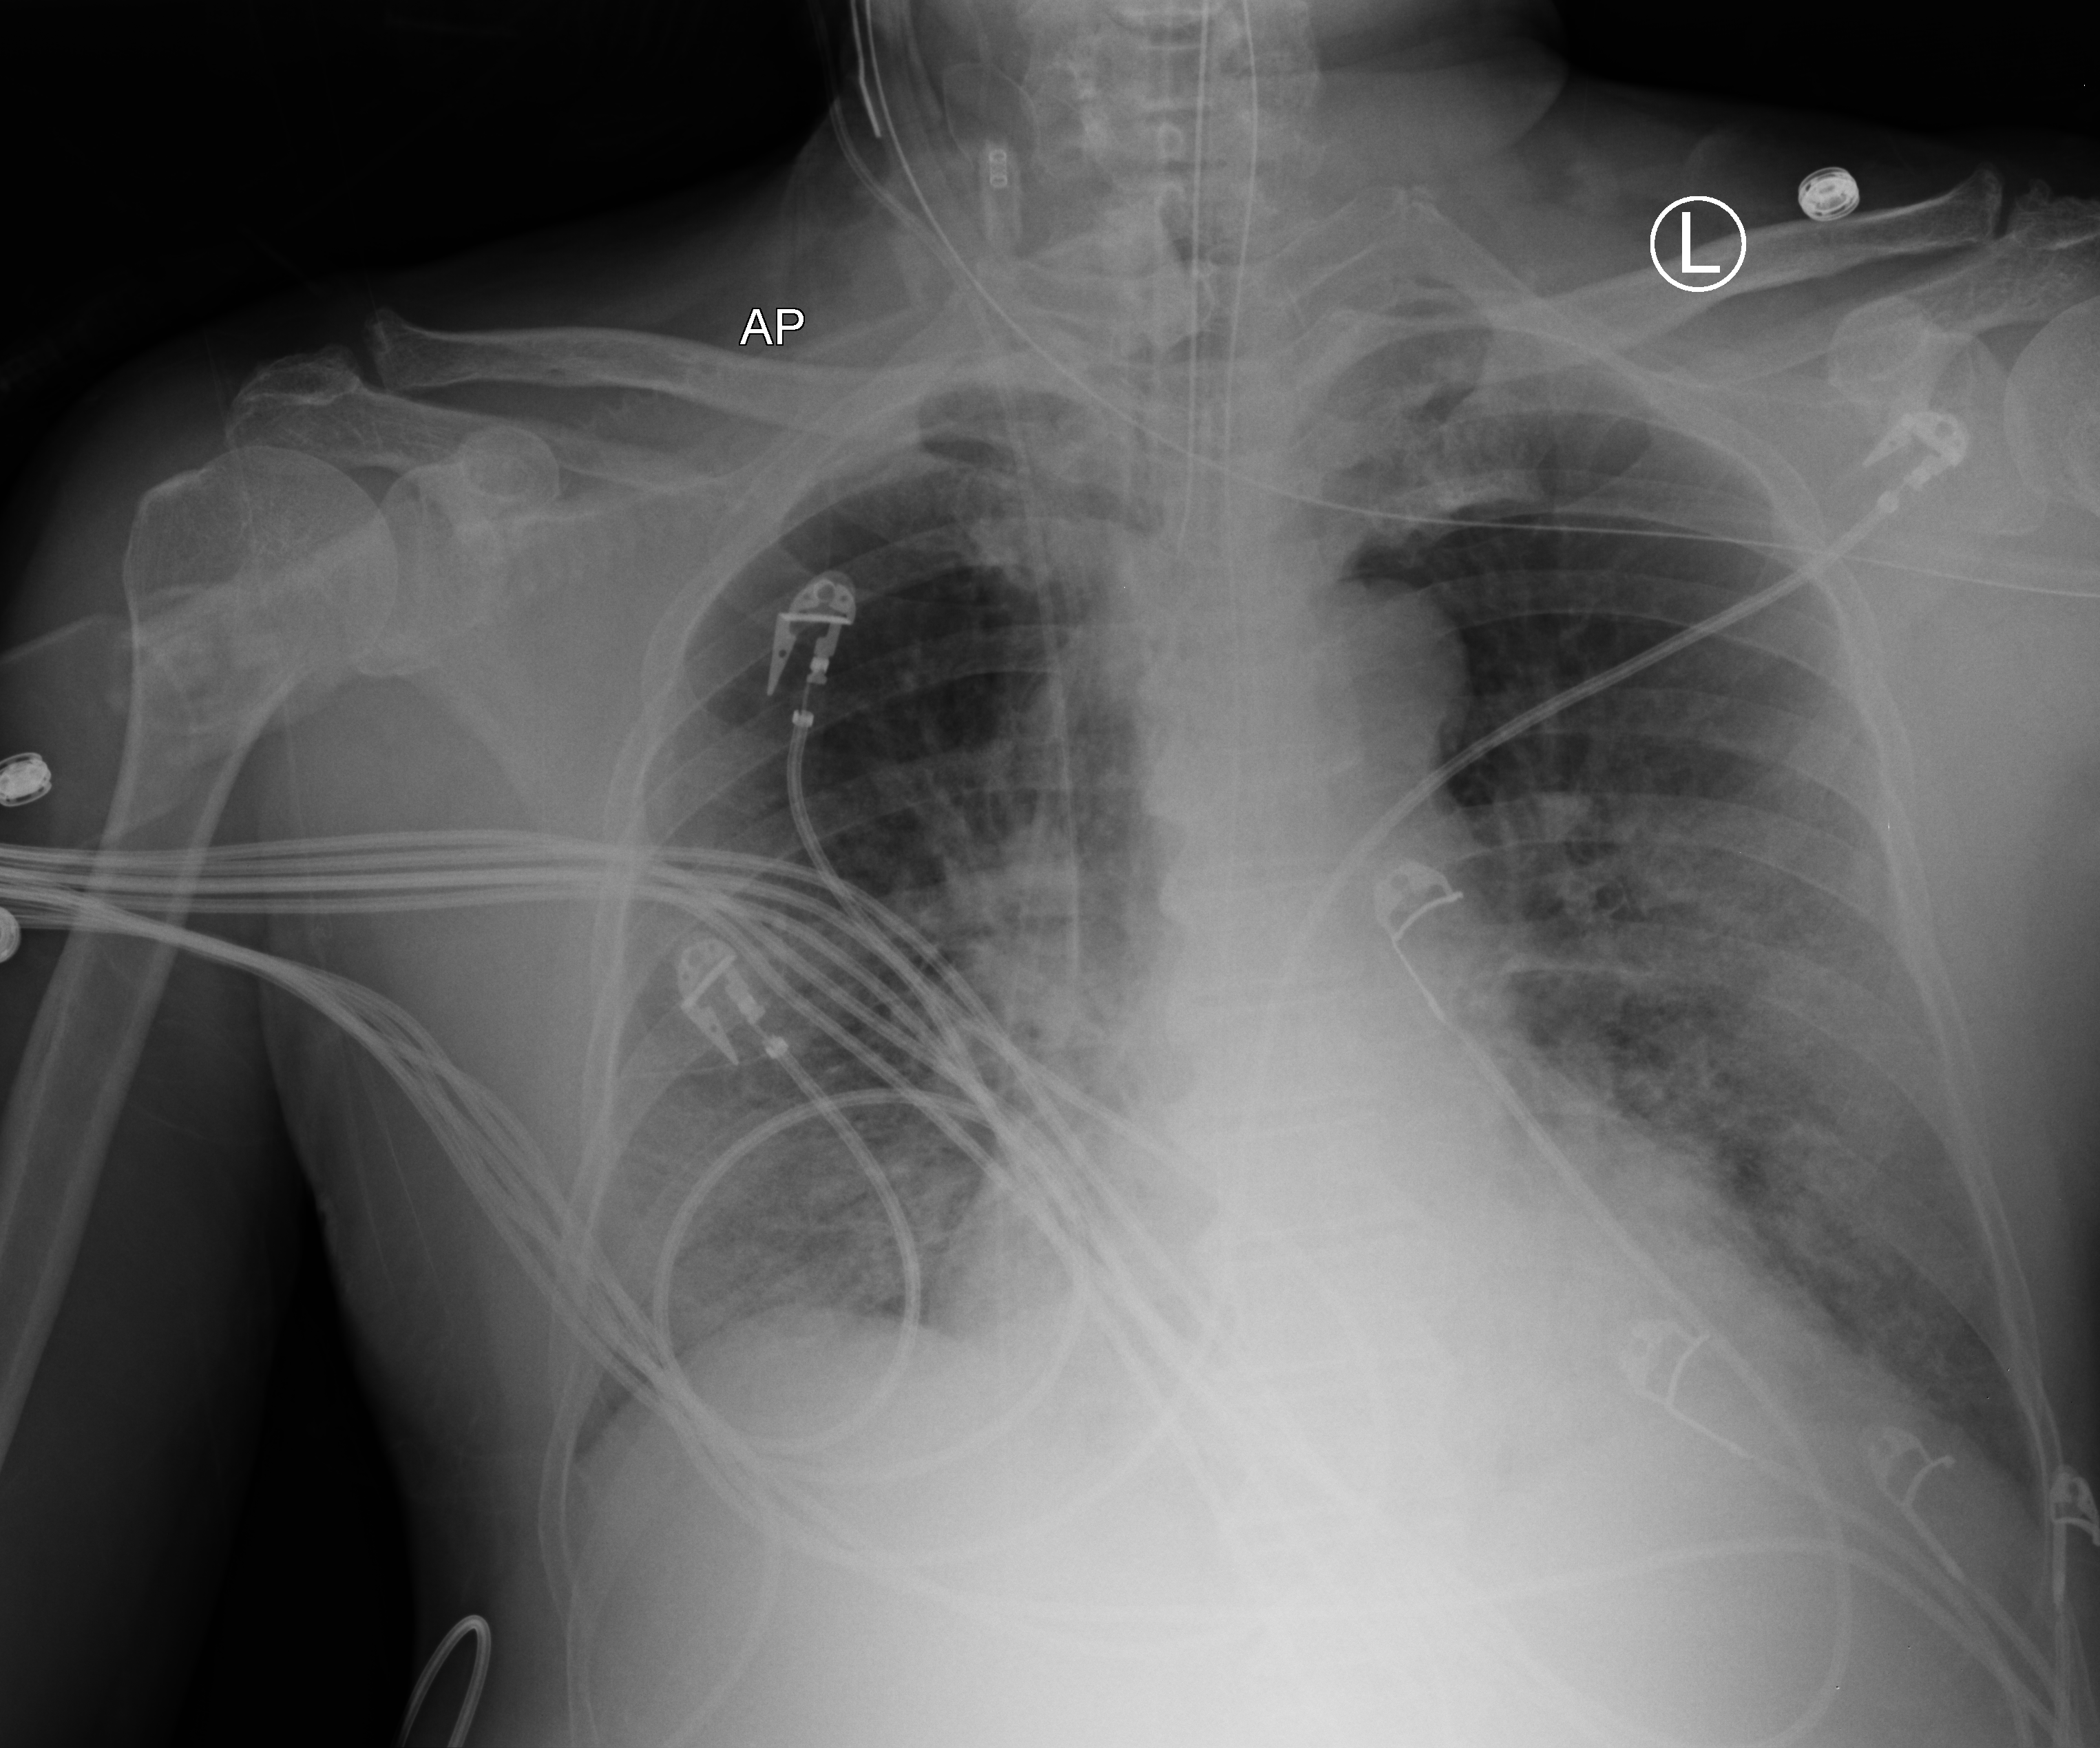
Portable chest radiograph; anteroposterior (AP) projection. Male patient hospitalised with COVID-19, age 60–74 years.
Hospital-stay facts (about this admission, not read from this image; timing relative to this image not recorded): chronic kidney disease (admission record): no.